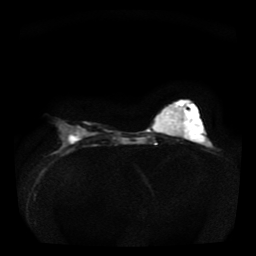
Breast MRI, one axial slice. Position 14 of 36 along the scan axis. Diffusion-weighted series; image 2 of 4 stored at this slice position (different b-values; order by instance number). 1.5 T. 5 mm slice thickness. 256 × 256 image matrix, field of view 330 × 330 mm. Female patient.
Outlined on this slice (expert manual segmentation):
- tumour on diffusion-weighted imaging: bounding box (x1, y1, x2, y2) in pixels: (67, 136, 78, 143)